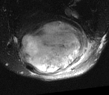
MRI of an extremity soft-tissue mass, one axial slice; slice 24 of 52 in the series (ordered by position); T2-weighted fat-saturated; MR volume resampled by the dataset authors to the PET/CT grid (not the native acquisition matrix); 3.27 mm slice thickness; 109 × 95 image matrix. Male patient. From the clinical record (not read from this slice): histological type: synovial sarcoma; site of the primary tumour: left poplietal fossa.
Structures marked on this image (expert contour drawn on MRI and transferred to this co-registered scan by the dataset authors):
- gross tumour volume (mass): bounding box (x1, y1, x2, y2) in pixels: (17, 17, 89, 75)